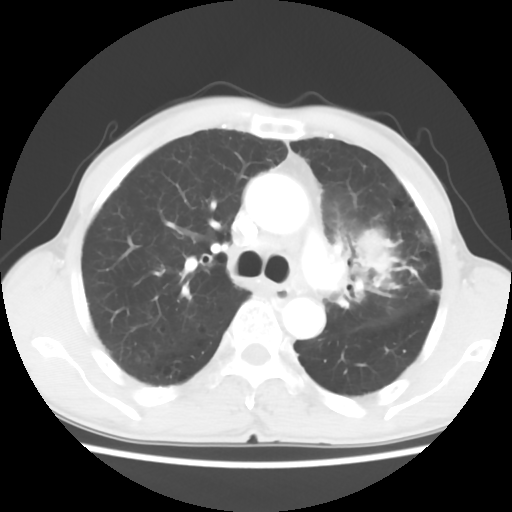
Chest CT, one axial slice. Position 39 of 60 along the scan axis. Reconstruction kernel STANDARD. Lung window (W 1500 / L -600 HU). 5 mm slice thickness. 512 × 512 image matrix, field of view 308 × 308 mm. Male patient, age 64 years. From the clinical record (not read from this slice): clinical TNM (as recorded): T3 N3 M0.
Structures marked on this image (bounding box drawn by a radiologist):
- lung tumour (recorded histology: adenocarcinoma): bounding box <348,215,413,316> (left, top, right, bottom; pixels)